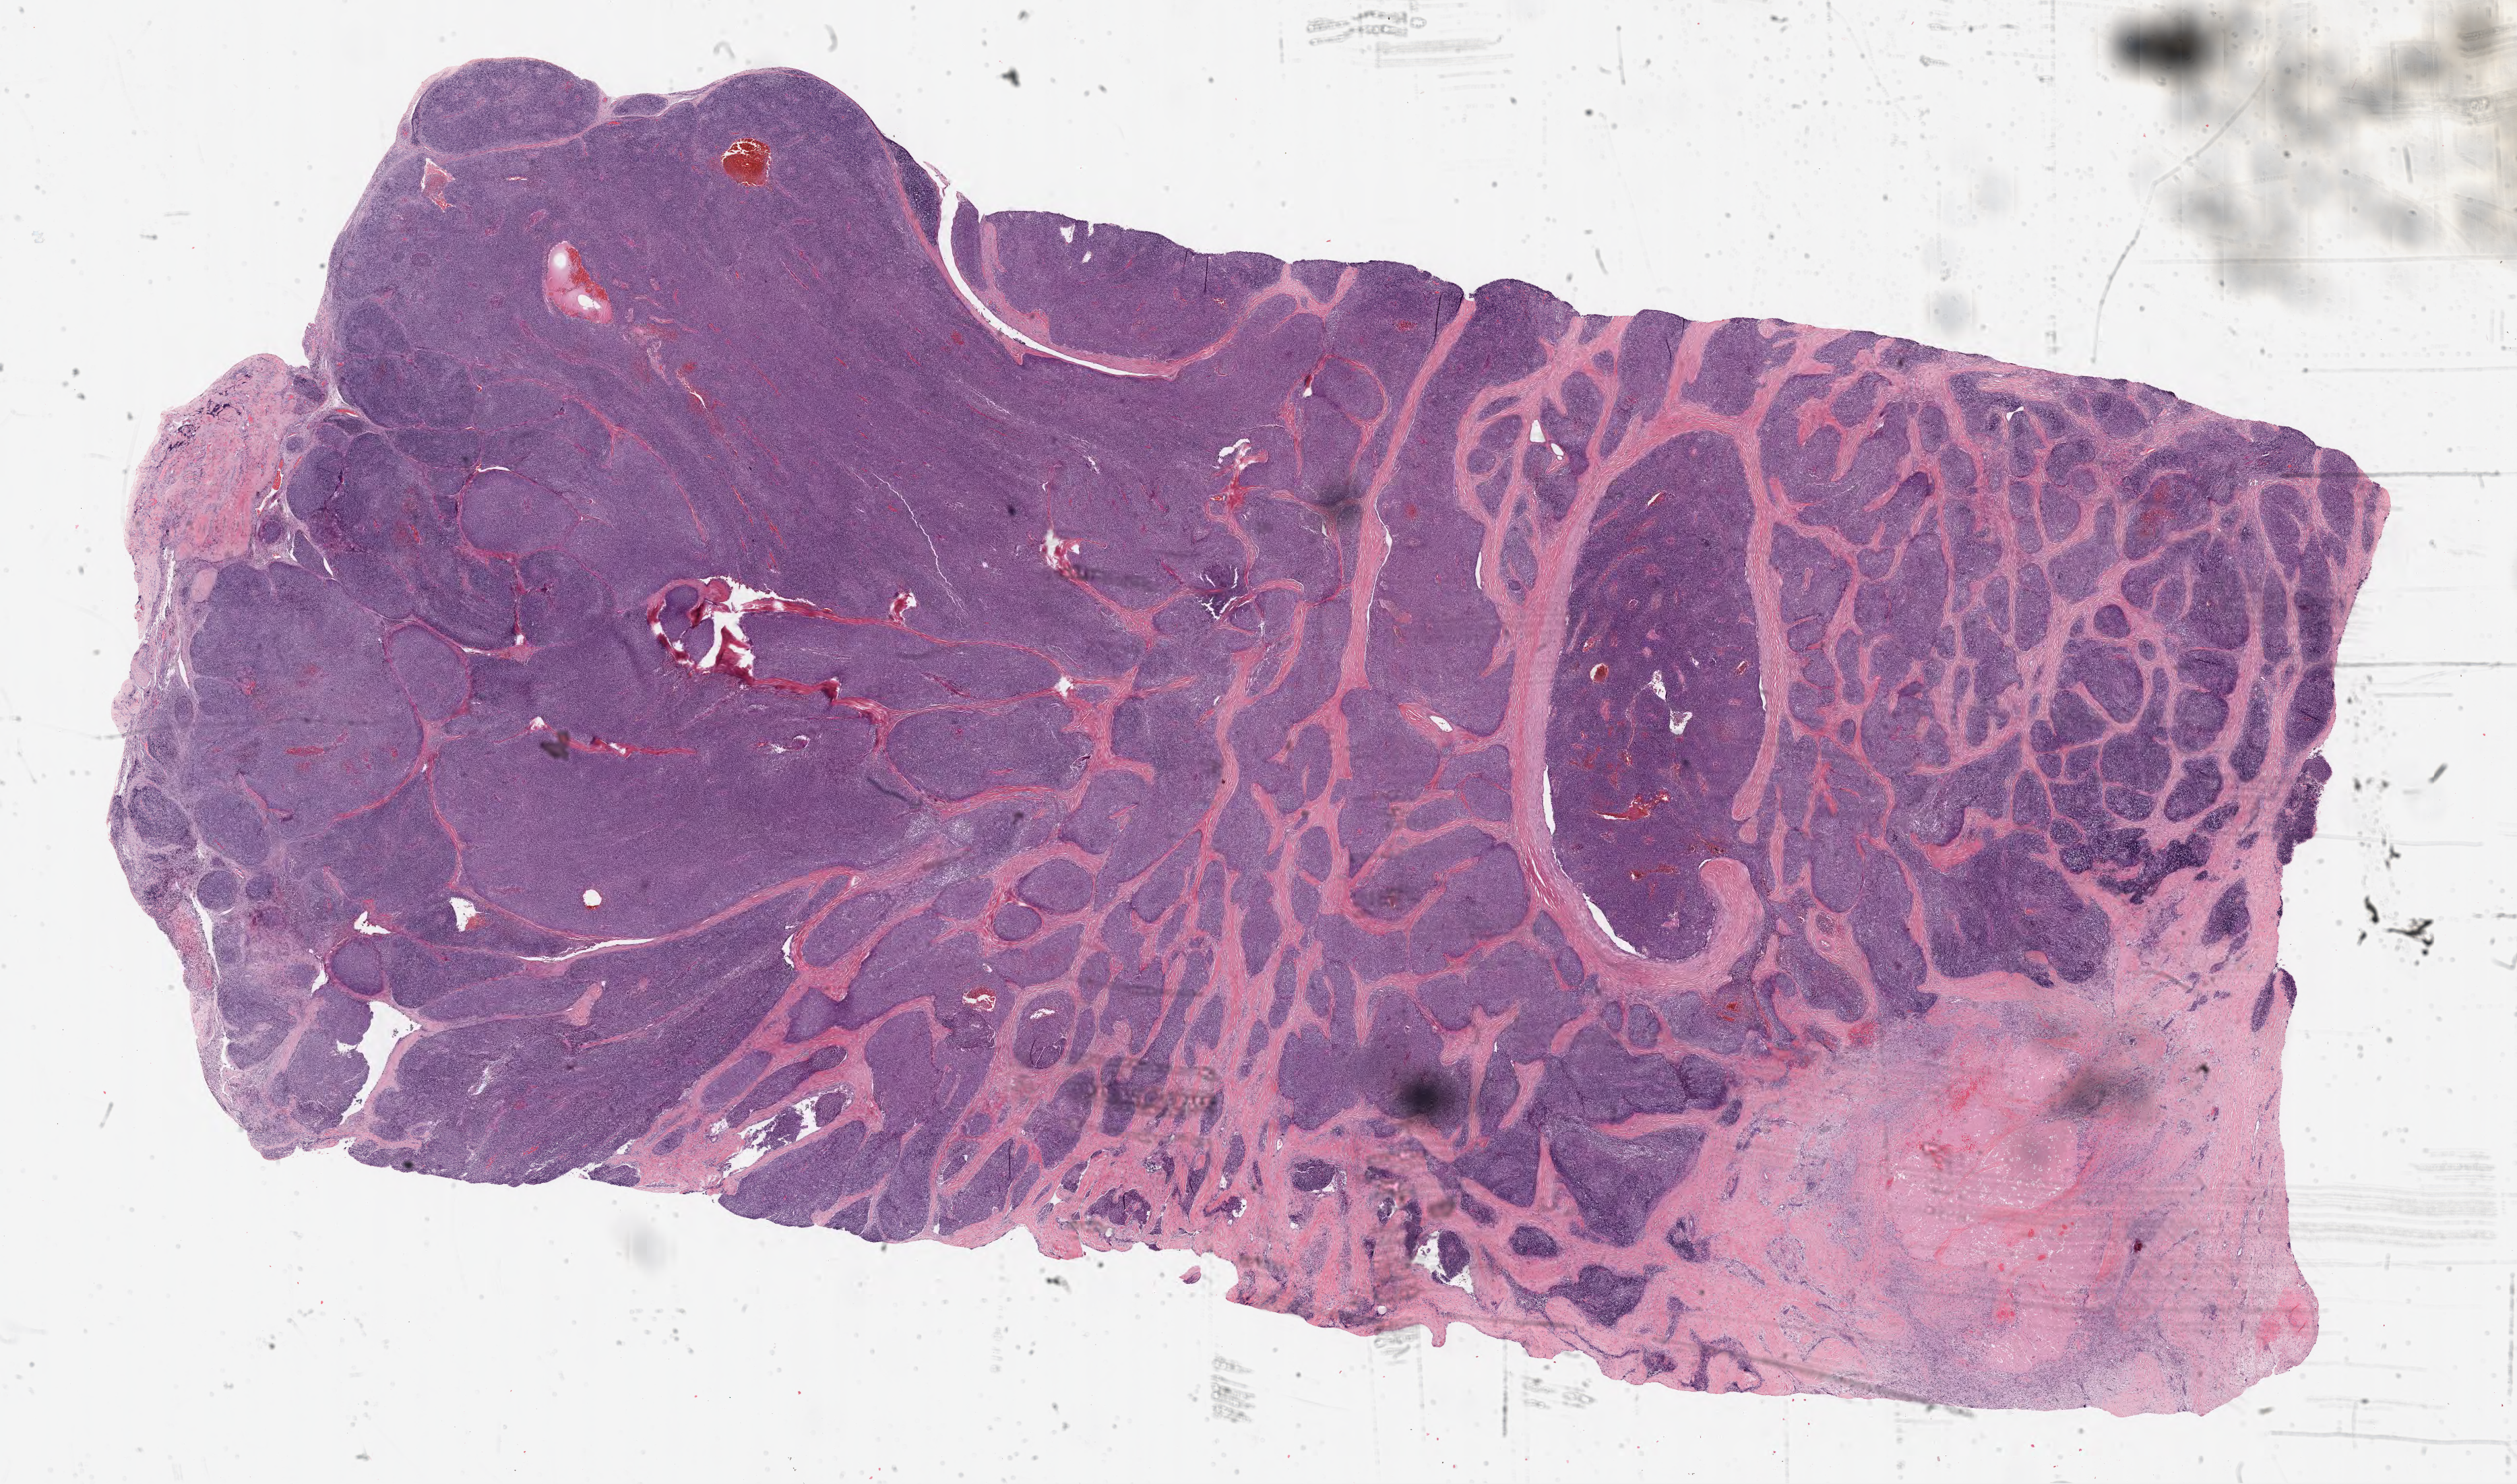
Whole-slide histology image, H&E-stained — shown as a low-resolution overview of the whole scanned area (about 30.2 x 17.8 mm, acquisition: 40x scan); formalin-fixed paraffin-embedded (FFPE) diagnostic section; sample: primary tumour, thymus. Patient: male, age at initial diagnosis 45 years.
* diagnosis: Thymoma, type B1, malignant